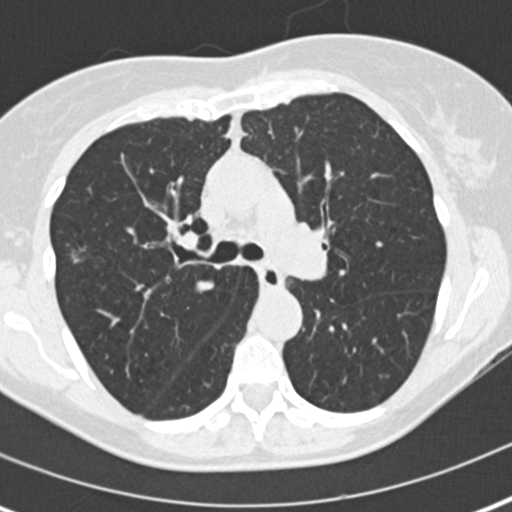
Low-dose screening chest CT, axial slice. Second screening round (one year after baseline). Lung window (W 1500 / L -600 HU). 512 × 512 image matrix, field of view 290 × 290 mm. Female participant, aged 60 years at enrolment. Current smoker at enrolment.
Lesion marked by an expert reader, bounding box (x1, y1, x2, y2) in pixels: (44, 227, 100, 279). The exam's reader record, not a measurement of the box and not confirmed to be the same lesion: non-calcified nodule or mass ≥4 mm, right upper lobe, 8 × 6 mm, spiculated (stellate) margins, soft tissue attenuation, pre-existing on the prior screen: no. Official screen result: positive, other. Lung cancer was diagnosed 511 days after this screen: bronchiolo-alveolar adenocarcinoma, NOS, right upper lobe, well differentiated (G1), stage IA (AJCC 6th edition), 11 mm at pathology.